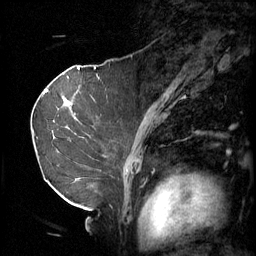
Breast MRI (dynamic contrast-enhanced), one sagittal slice. Position 35 of 60 along the scan axis. 3 images stored at this slice position (order not interpretable as contrast timing). 1.5 T. TE 4.2 ms, TR 11 ms. 2 mm slice thickness. 256 × 256 image matrix, field of view 220 × 220 mm. Female patient, age 69 years.
Outlined on this slice (semi-automatically segmented with operator editing):
- analysis volume of interest (the breast-tissue region the enhancement analysis was run in; not a lesion): bounding box <36,88,106,189> (left, top, right, bottom; pixels)
- tumour enhancement mask (voxels above the 70 % enhancement threshold inside the analysis volume of interest): <65,100,76,119>